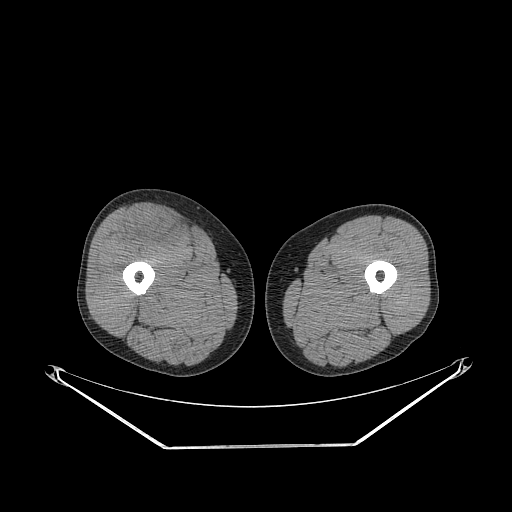
CT of an extremity soft-tissue mass (from a PET/CT study), one axial slice. Reconstruction kernel STANDARD. Soft-tissue window (W 400 / L 40 HU). 3.75 mm slice thickness. 512 × 512 image matrix, field of view 500 × 500 mm. Male patient. Case-level facts recorded for this patient, not image findings: histological type: pleiomorphic leiomyosarcoma; grade: intermediate; site of the primary tumour: right thigh.
Structures marked on this image (expert contour drawn on MRI and transferred to this co-registered scan by the dataset authors):
- gross tumour volume including surrounding oedema: box from (x=126, y=208) to (x=179, y=243) px
- gross tumour volume (mass): (x=142, y=215)–(x=174, y=239)